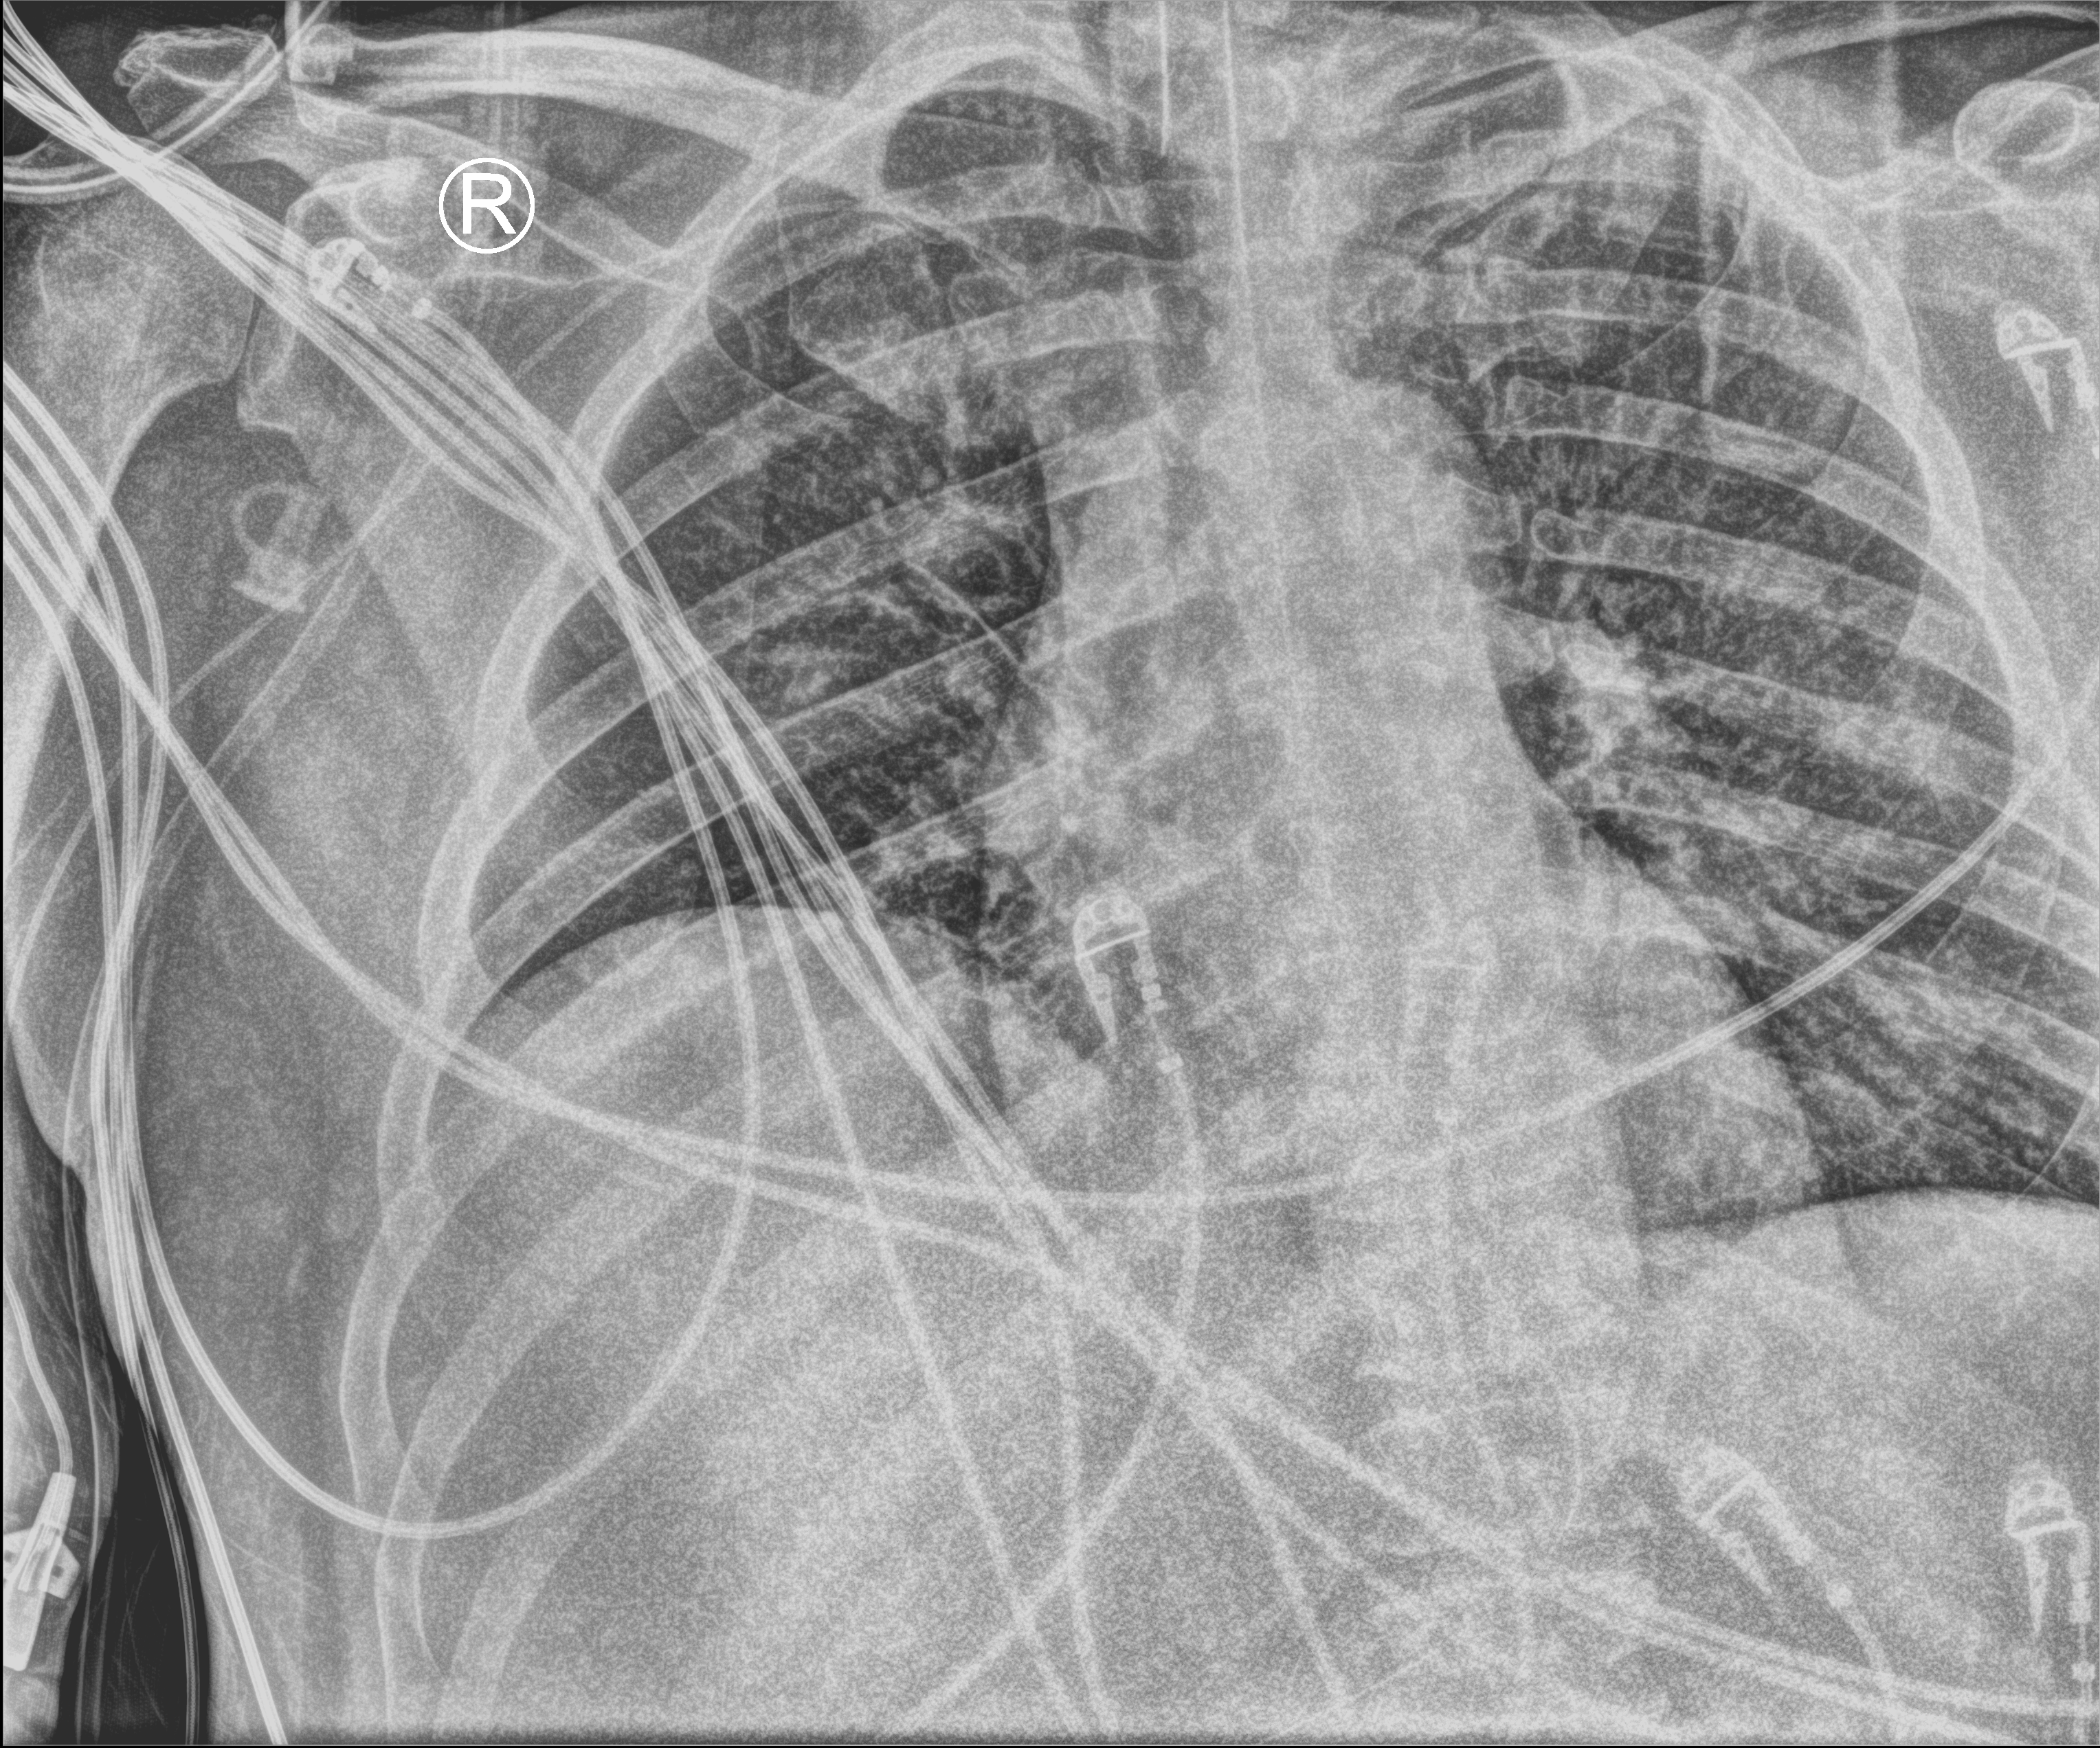
Portable chest radiograph, anteroposterior (AP) projection. Patient hospitalised with COVID-19; male, aged 18–59 years.
Admission-level facts for this patient (not findings on this image; timing relative to this image not recorded): mechanically ventilated during this hospital stay: yes; admitted to intensive care during this hospital stay: yes.